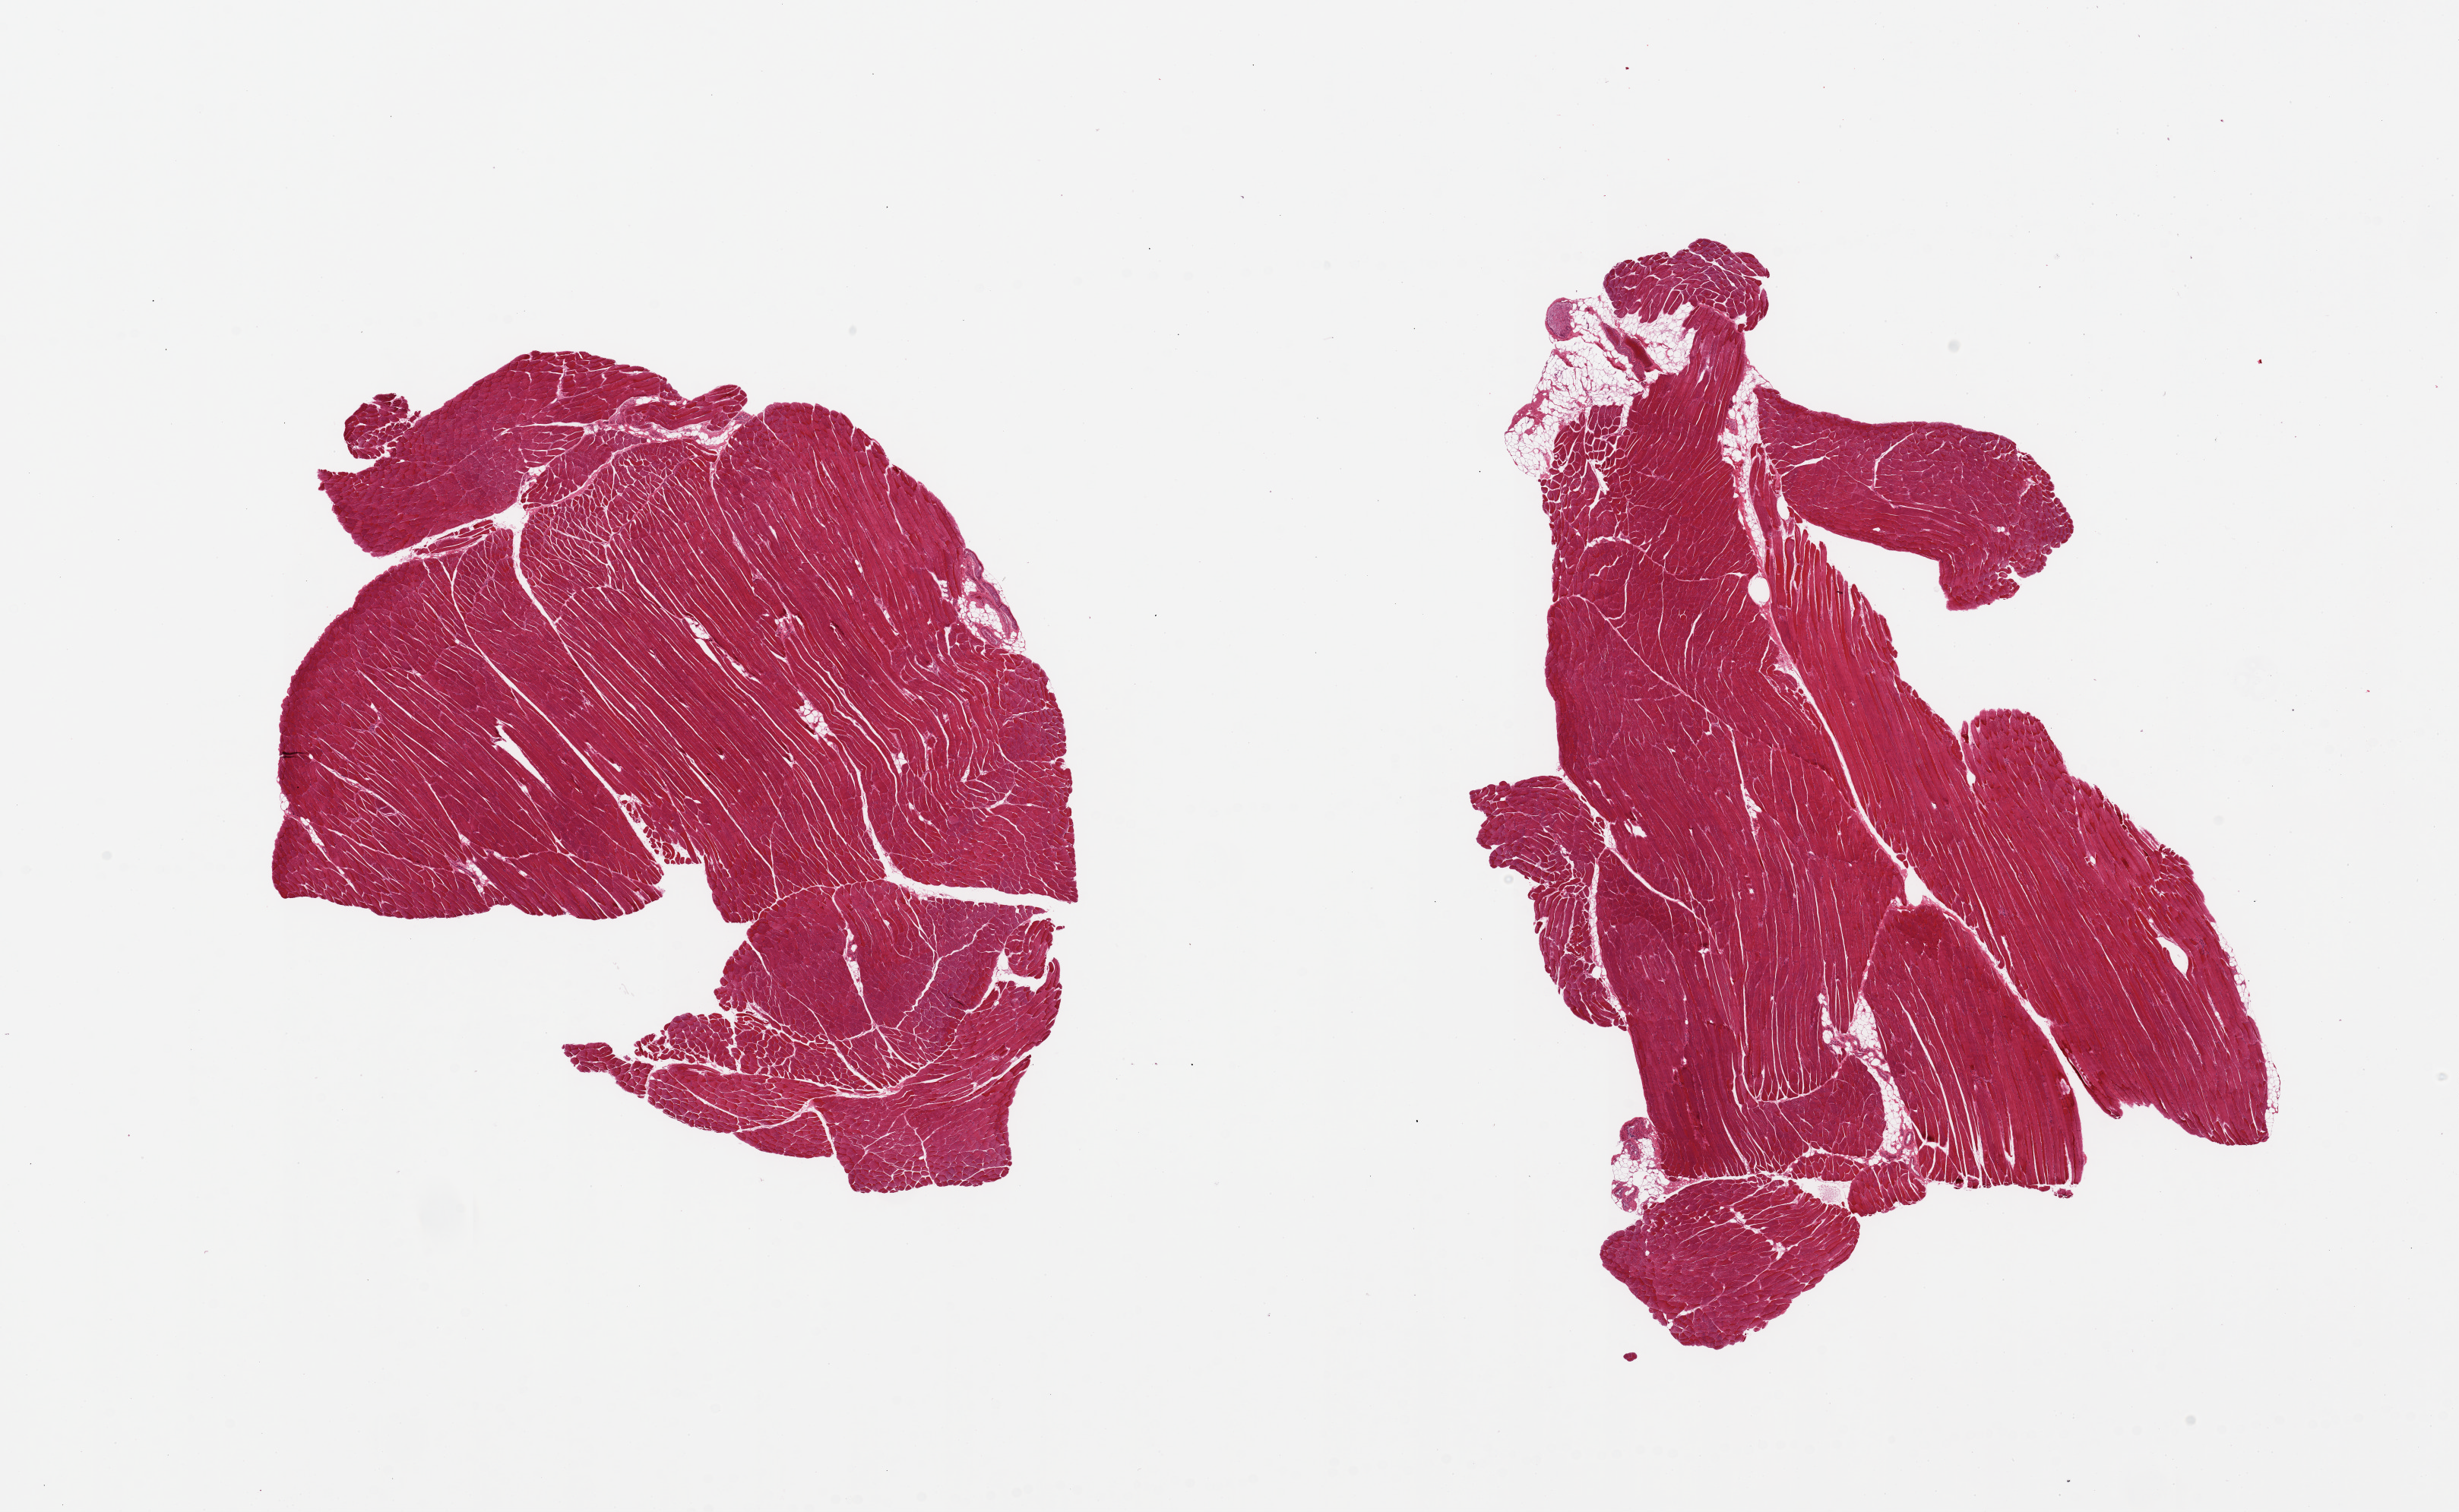
Digitized H&E-stained section, low-resolution overview of the scanned area, about 25.6 x 15.7 mm; PAXgene-fixed, paraffin-embedded tissue; sampled site (target tissue): skeletal muscle; tissue donor sample.
Pathologist's review note for this sample: 2 pieces, minimal interstitial fat.